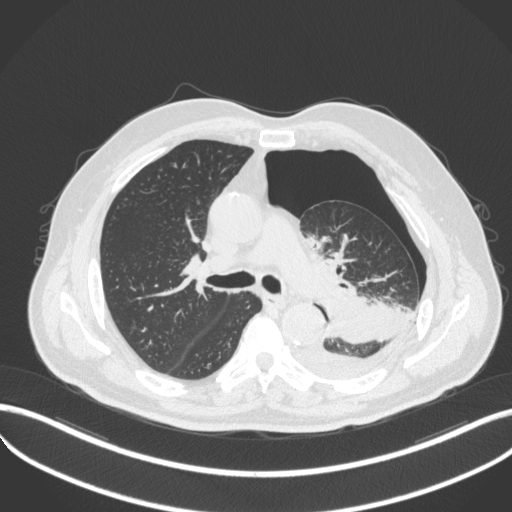
Chest CT, one axial slice; position 325 of 466 along the scan axis; reconstruction kernel B31f; lung window (W 1500 / L -600 HU); 512 × 512 image matrix, field of view 400 × 400 mm. Patient: male, 76 years. Case-level facts recorded for this patient, not image findings: clinical TNM (as recorded): T3 N0 M1b.
Structures marked on this image (rectangle marked by the reading radiologist):
- lung tumour (recorded histology: adenocarcinoma): bounding box [x1, y1, x2, y2] px = [321, 292, 395, 351]